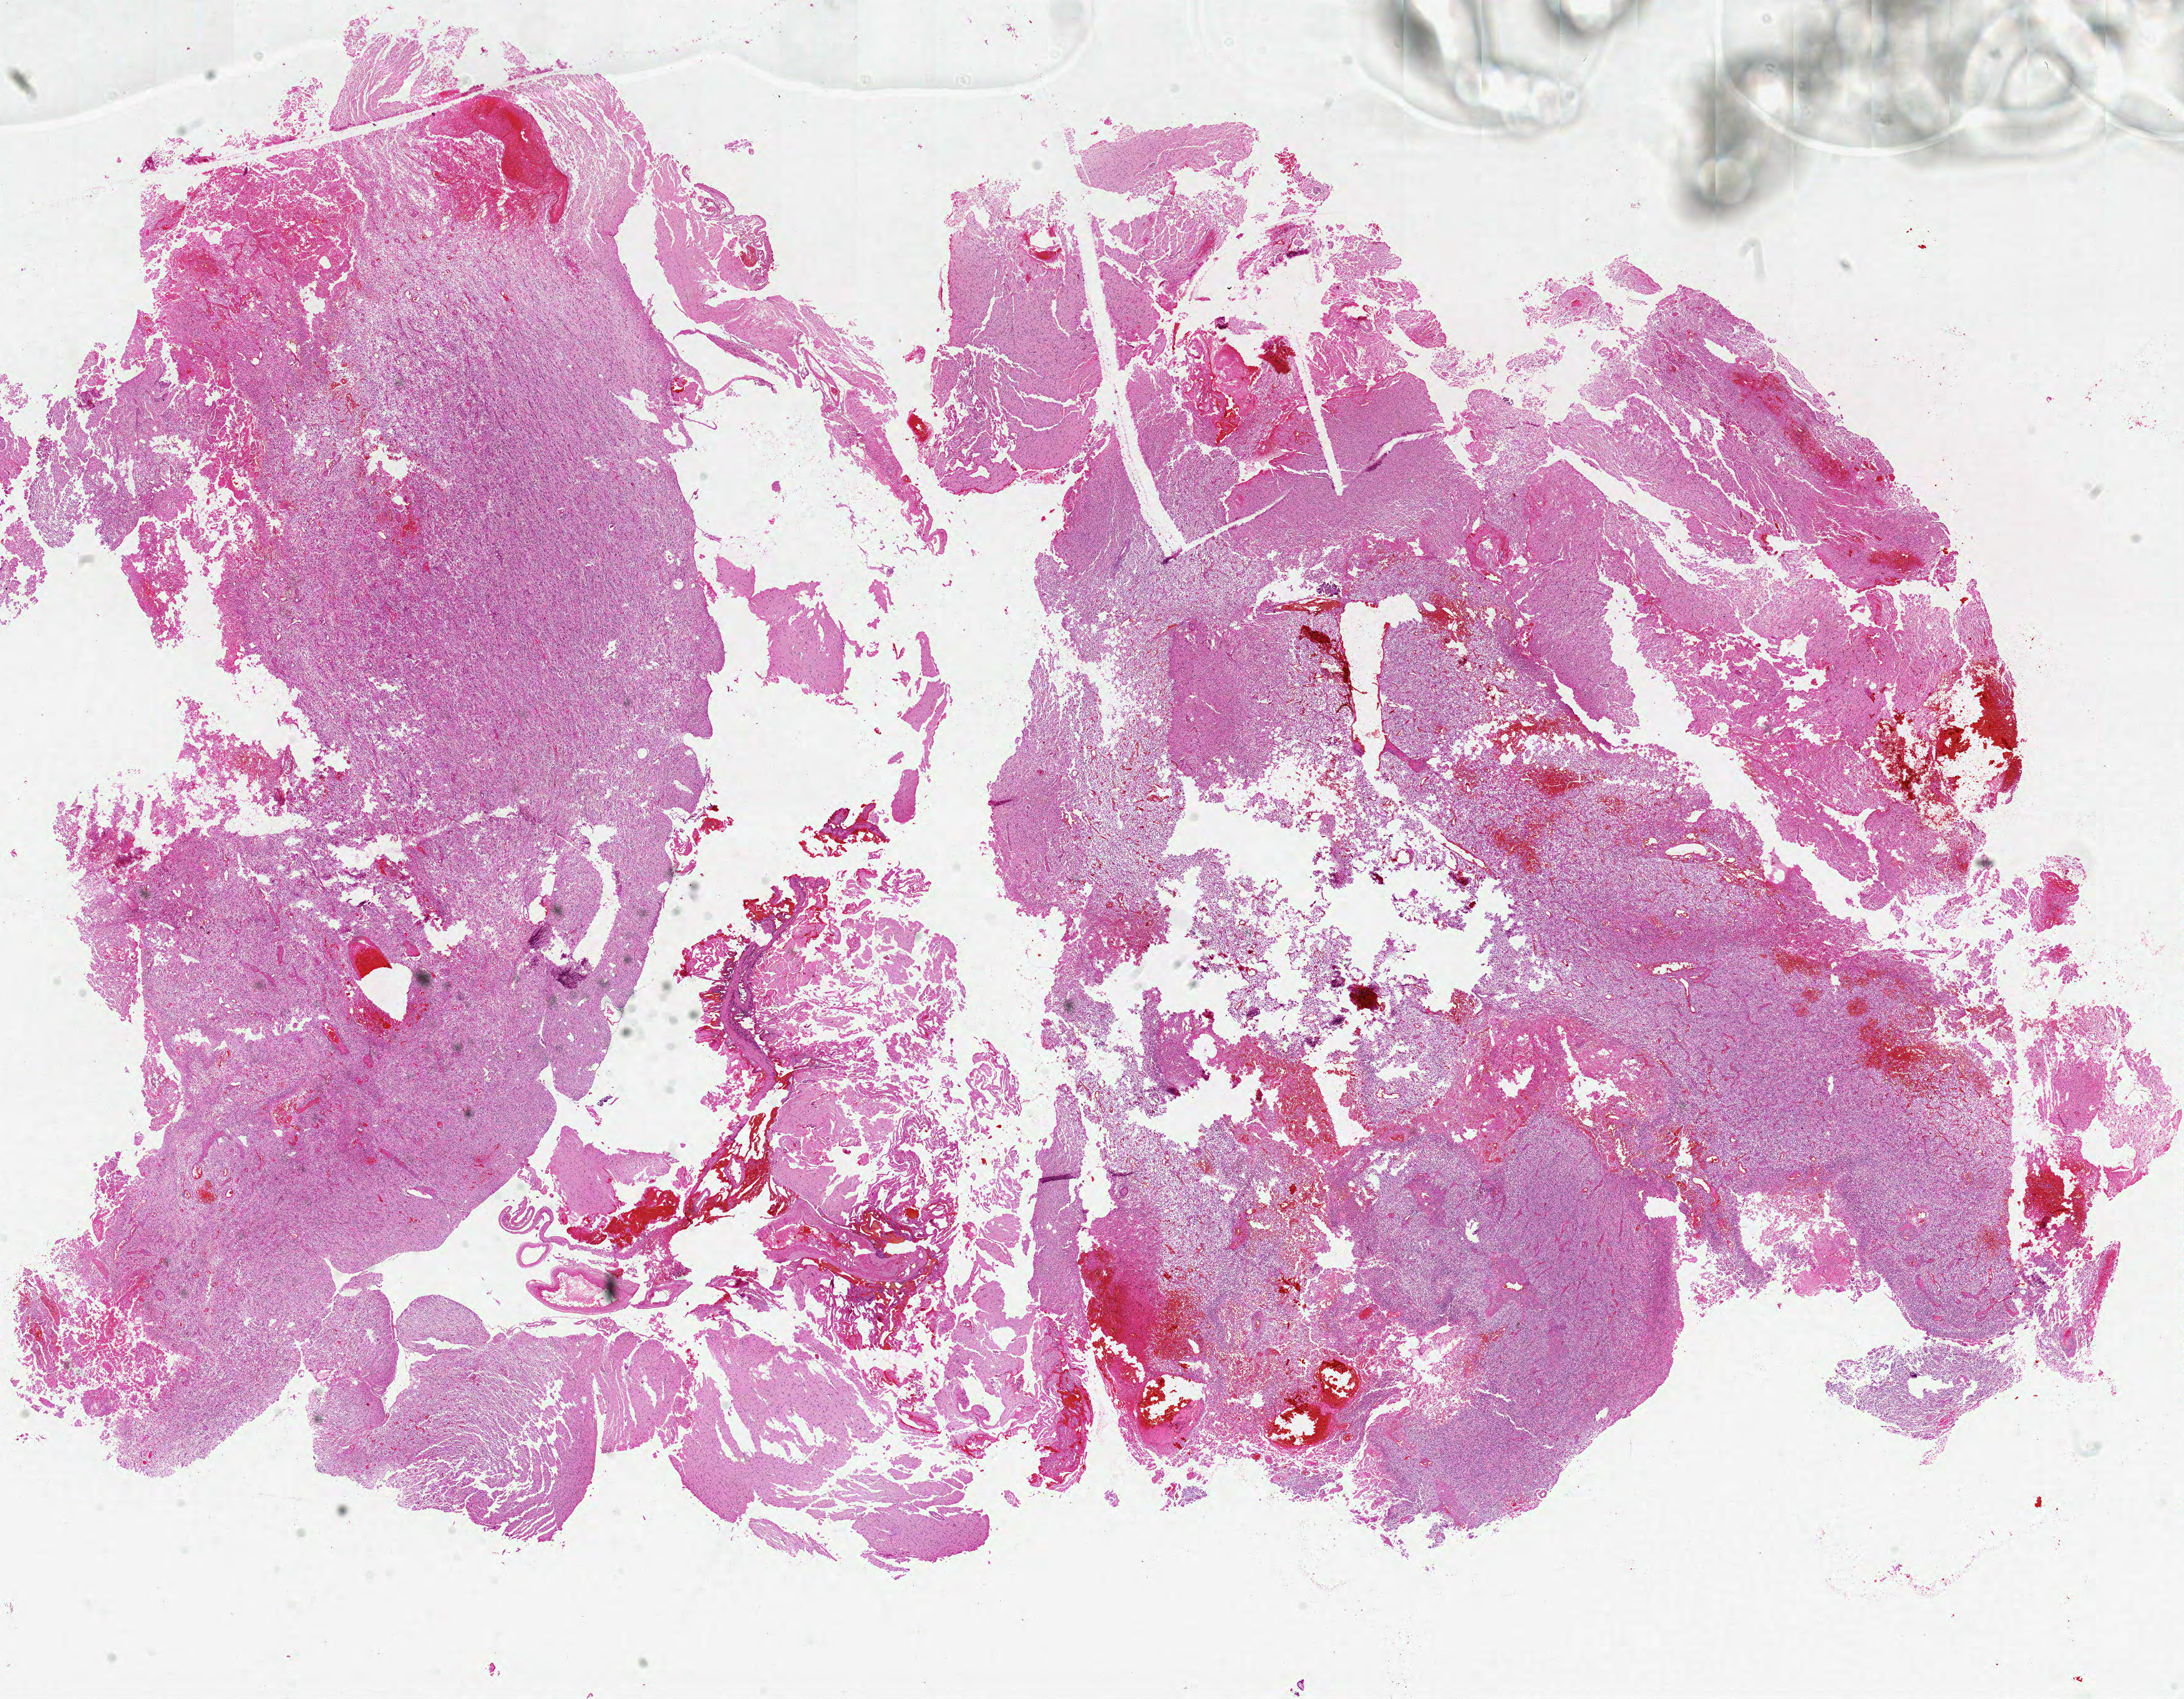
Whole-slide histology image, H&E, low-resolution overview of the scanned area, about 28.0 x 21.8 mm (from a 20x scan); formalin-fixed paraffin-embedded (FFPE) diagnostic section; sample: primary tumour, brain. Male, age 53 years at initial diagnosis.
Diagnosis: Glioblastoma.